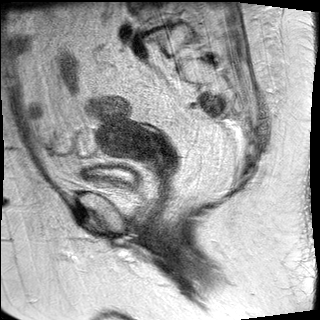
Pelvic MRI for cervical cancer, one sagittal slice; slice 11 of 27 in the series (ordered by position); T2-weighted; 1.5 T; TE 89 ms, TR 2740 ms; 4 mm slice thickness; 320 × 320 image matrix. Patient: female, 67 years.
Outlined on this slice (manually delineated by an expert):
- uterus and cervix: box from (x=96, y=116) to (x=179, y=178) px